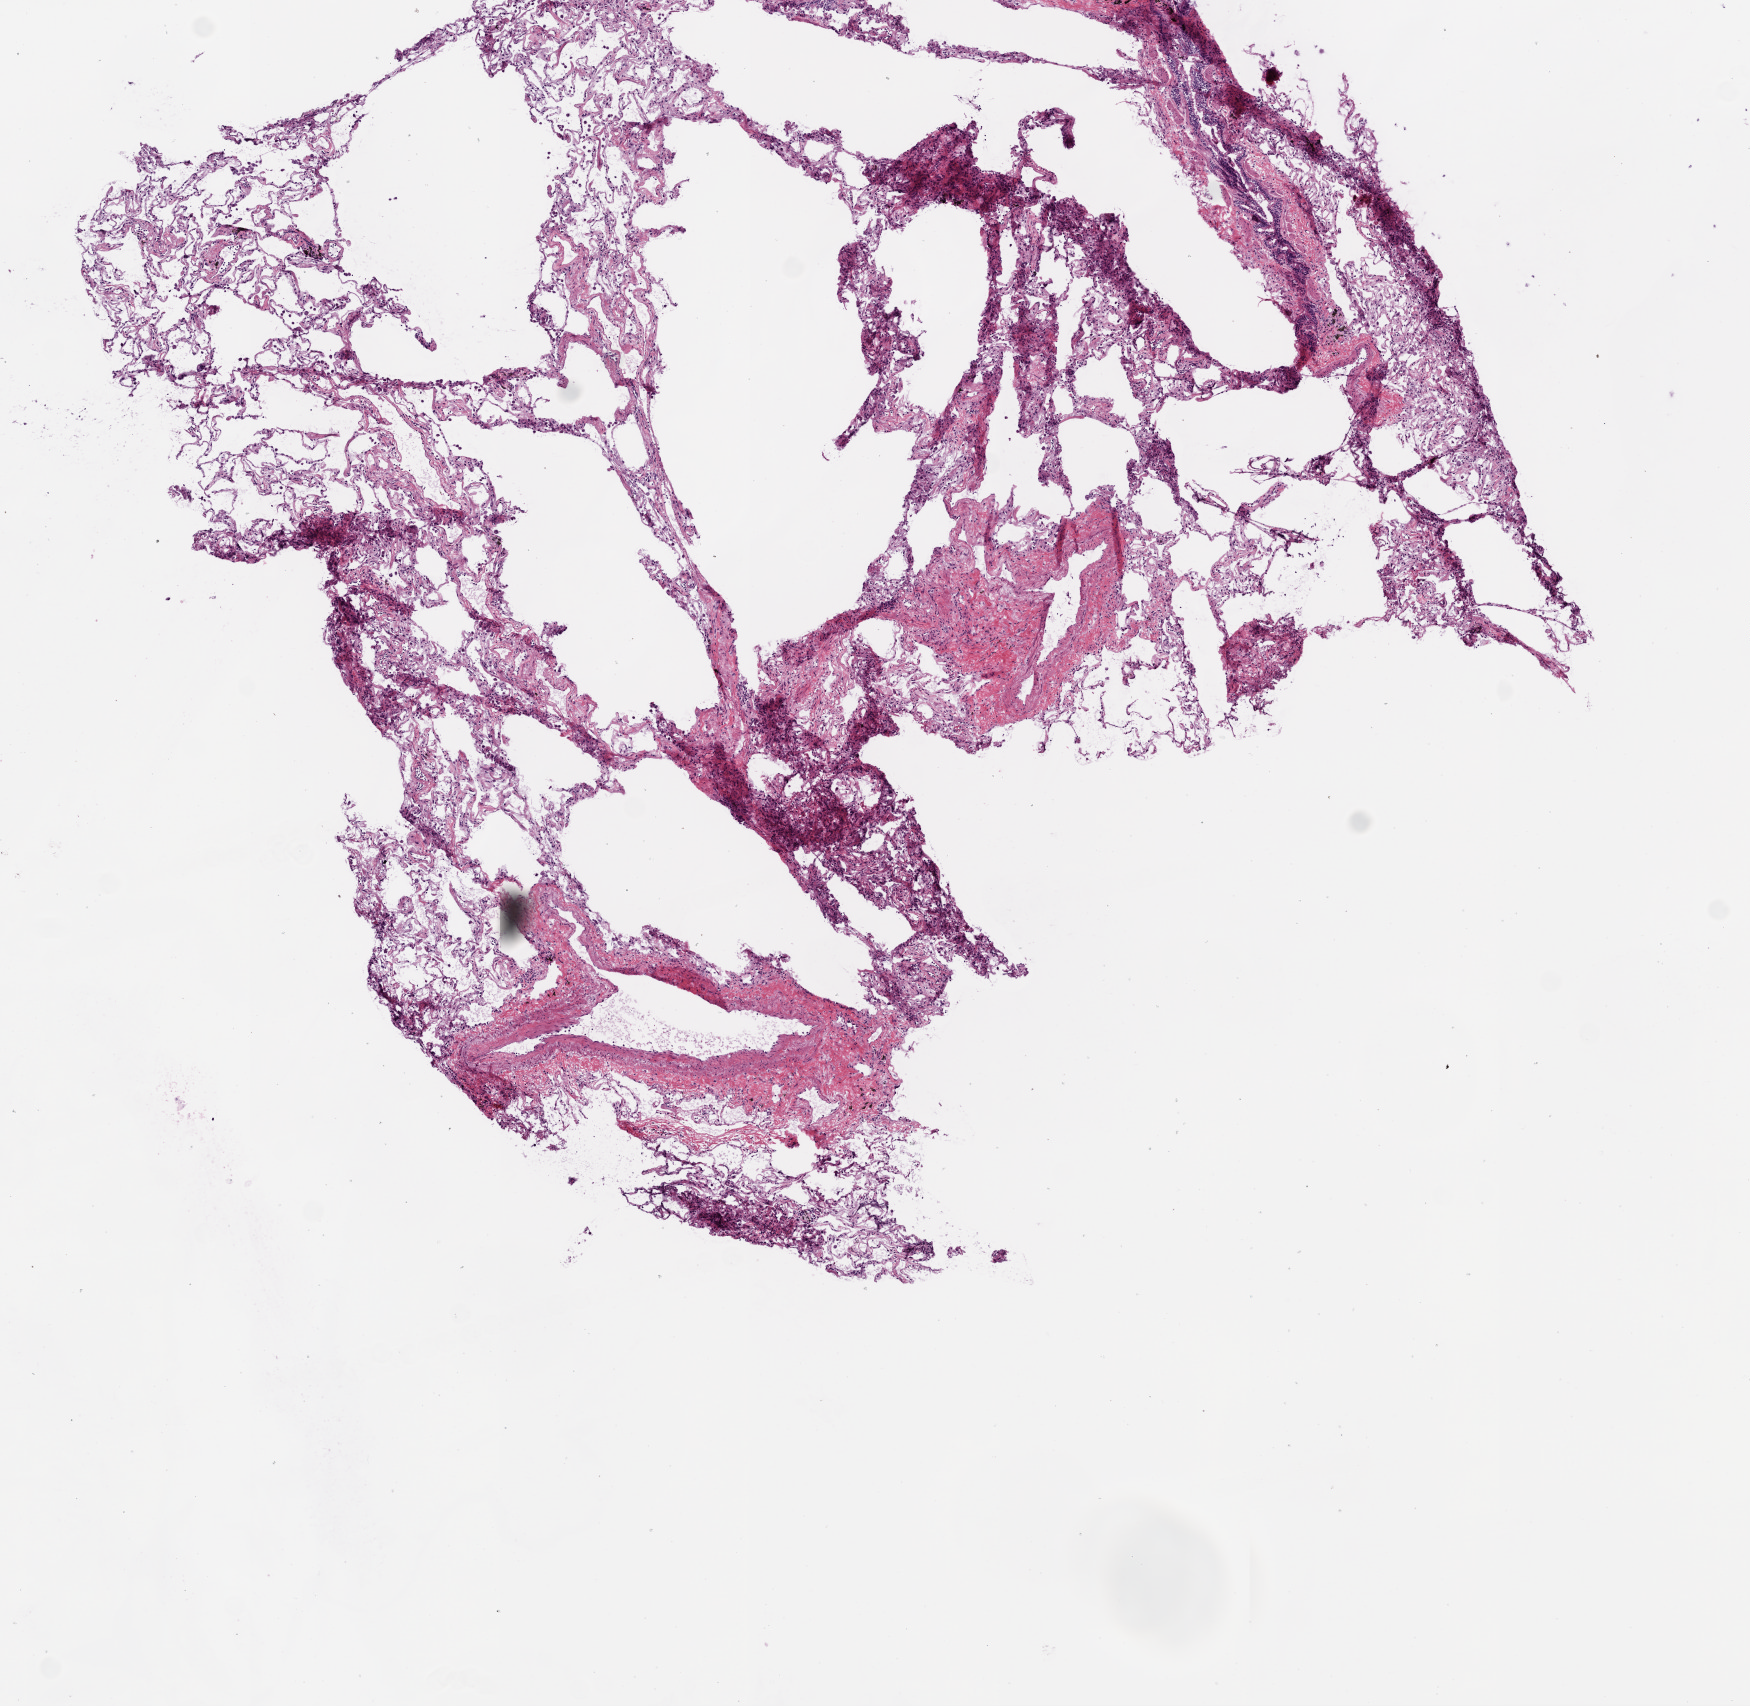
Whole-slide histology image, H&E — whole scanned area (about 7.0 x 6.8 mm, acquisition: 20x scan) shown as a low-resolution overview, frozen section from the top of the tissue portion, solid tissue normal (non-tumour tissue) sample from the lung. Female, age 65 years at initial diagnosis.
This section: solid tissue normal (non-tumour) sample from the same patient. Patient diagnosis: Adenocarcinoma, NOS (upper lobe, lung).